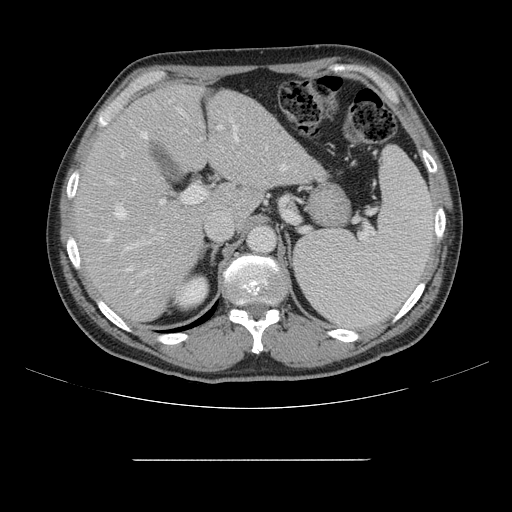
Contrast-enhanced abdominal CT, one axial slice; 120 kVp; intravenous contrast given; soft-tissue window (W 400 / L 40 HU); 2.5 mm slice thickness; 512 × 512 image matrix, field of view 404 × 404 mm. Male patient, age 54 years. From the clinical record (not read from this slice): diagnosis: colorectal cancer liver metastases, imaged before liver resection; multiple liver metastases: yes; largest metastasis: 1 cm; chemotherapy before resection: yes.
Structures marked on this image (outlined manually by an expert reader):
- hepatic veins: bounding box [x1, y1, x2, y2] px = [105, 129, 288, 272]
- liver: [77, 85, 322, 323]
- planned liver remnant (the part of the liver to remain after resection): [77, 85, 237, 322]
- portal vein (with intrahepatic branches): [119, 99, 237, 302]